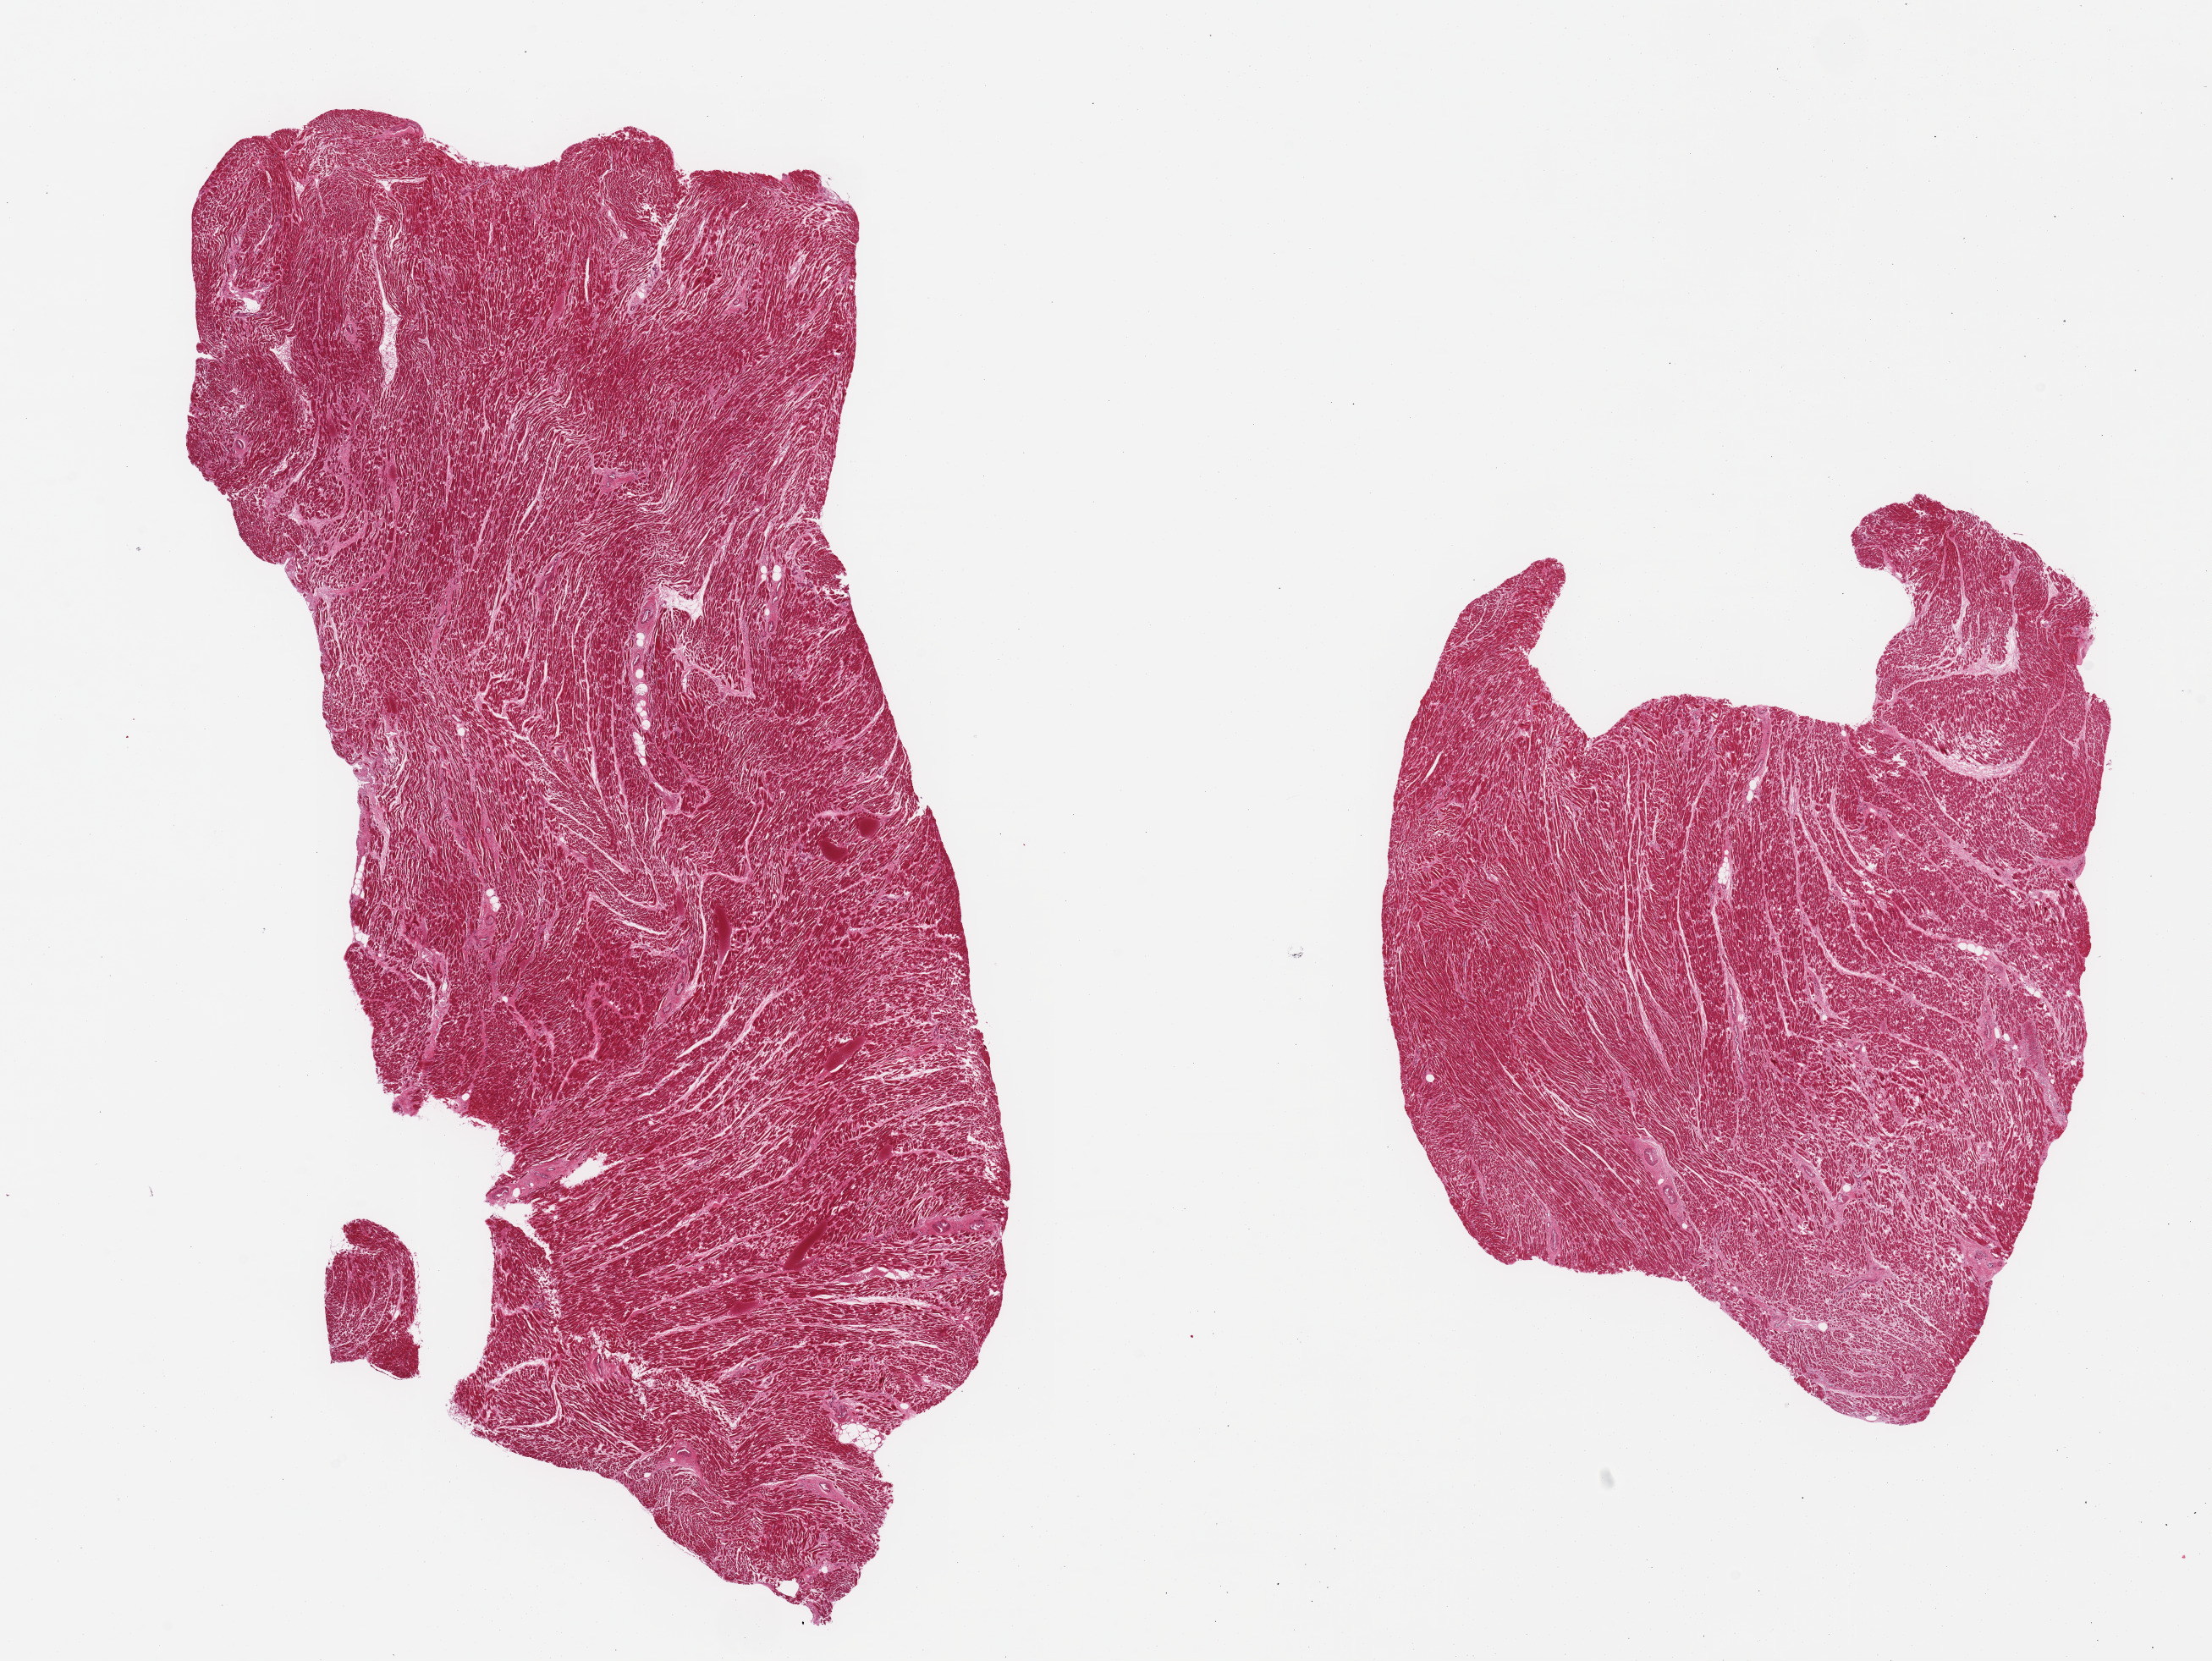
Digitized haematoxylin and eosin-stained section, shown as a low-resolution overview of the whole scanned area (about 20.7 x 15.5 mm, slide scanned at 20x), PAXgene-fixed, paraffin-embedded tissue, sampled site (target tissue): heart, tissue donor sample. Male donor.
* reviewer comment on this tissue sample: 2 pieces, moderate-marked interstitial fibrosis/chronic ischemic changes